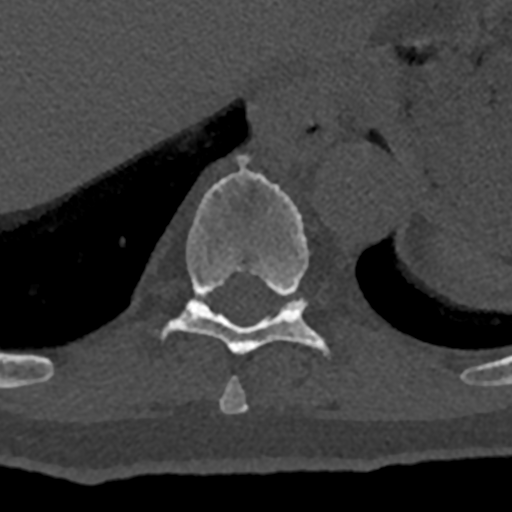
CT including the spine, one axial slice. Position 600 of 797 along the scan axis. 120 kVp. Bone window (W 1800 / L 400 HU). 0.5 mm slice thickness. 512 × 512 image matrix, field of view 160 × 160 mm. Patient: male, 74 years. From the clinical record (not read from this slice): primary cancer: renal.
Structures marked on this image (semi-automatic segmentation, software-assisted and operator-edited):
- T10 vertebra: box from (x=158, y=155) to (x=330, y=355) px
- T11 vertebra: (x=283, y=298)–(x=307, y=310)
- T9 vertebra: (x=219, y=377)–(x=248, y=413)